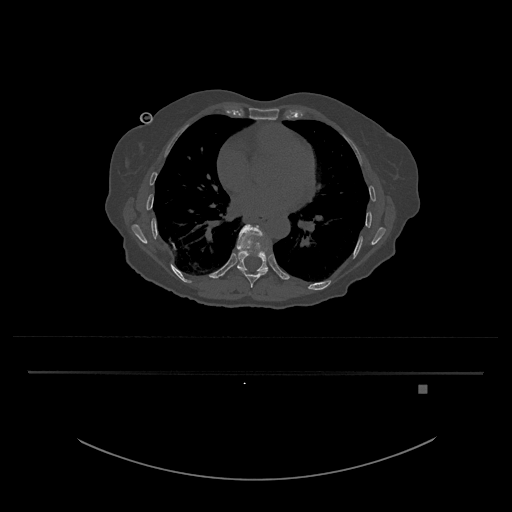
CT including the spine, one axial slice. Position 739 of 797 along the scan axis. Reconstruction kernel Br40s/3. Bone window (W 1800 / L 400 HU). 0.5 mm slice thickness. 512 × 512 image matrix, field of view 500 × 500 mm. Female patient, age 57 years. From the clinical record (not read from this slice): primary cancer: cervical.
Annotated regions visible in this slice (semi-automatic segmentation, software-assisted and operator-edited):
- T10 vertebra: bounding box (x1, y1, x2, y2) in pixels: (228, 224, 269, 277)
- T9 vertebra: (240, 270, 267, 288)